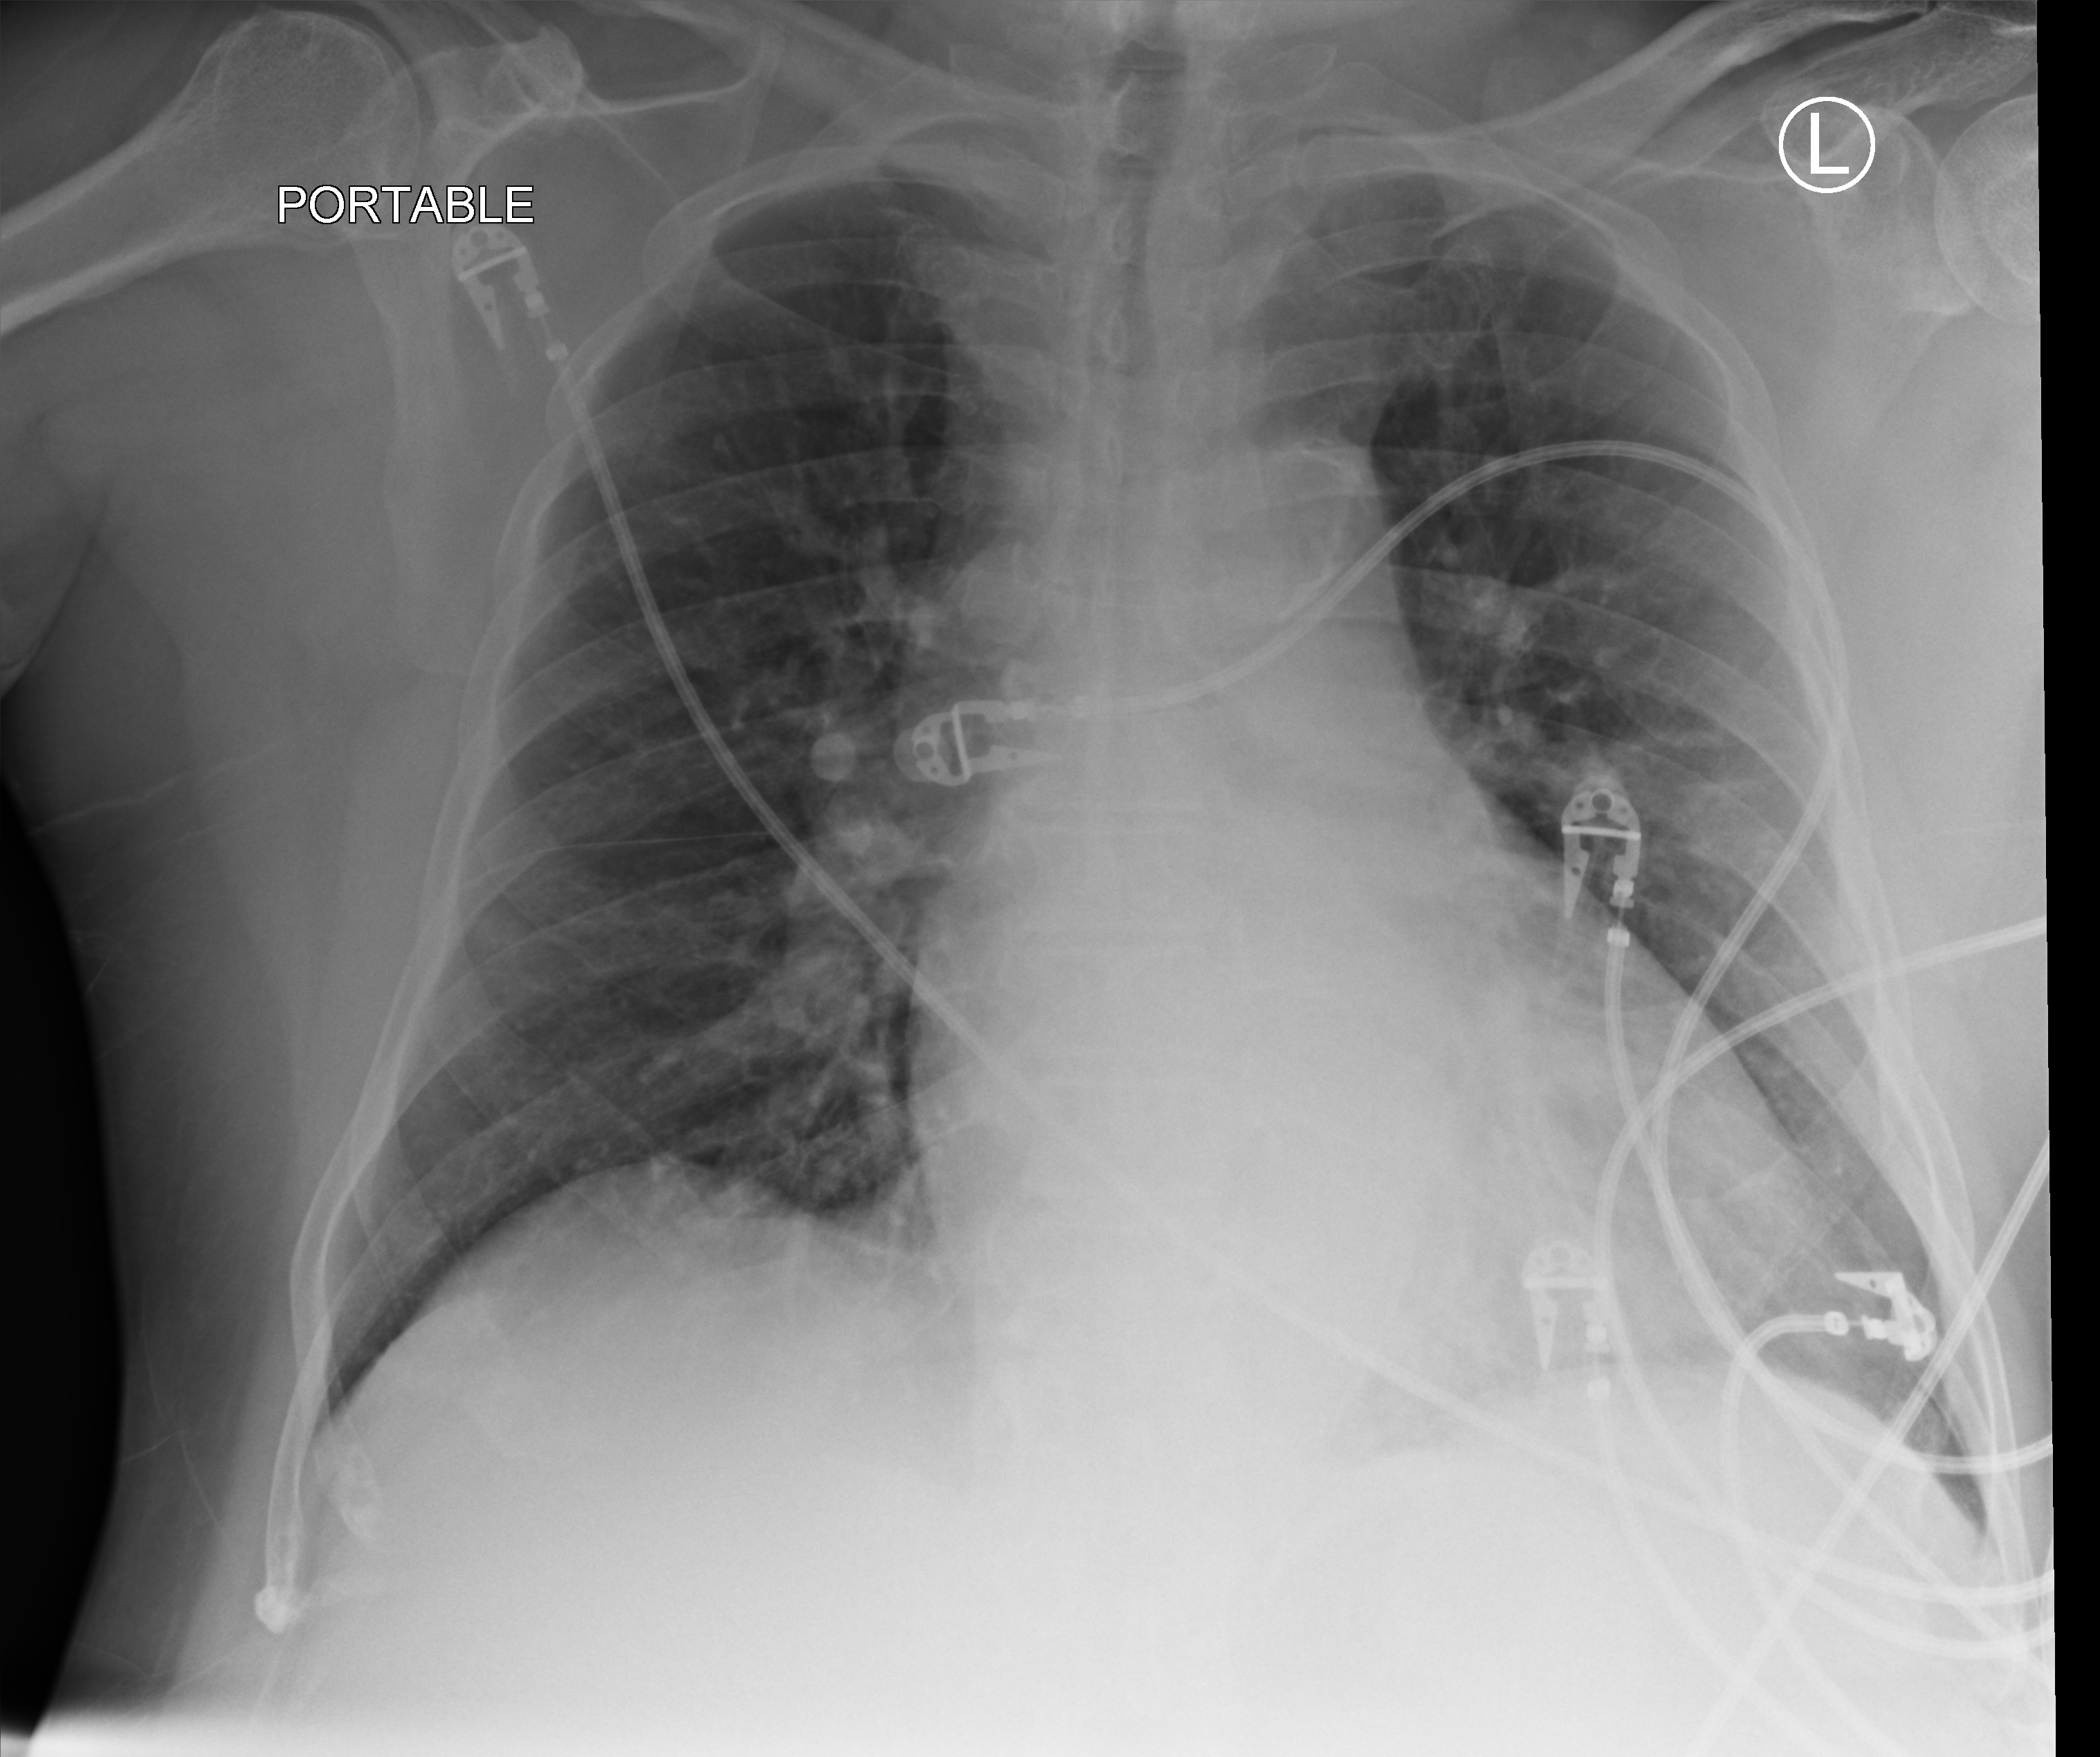
Portable chest radiograph; anteroposterior (AP) projection. Patient hospitalised with COVID-19; male, aged 60–74 years.
Admission-level facts for this patient (not findings on this image; timing relative to this image not recorded): mechanically ventilated during this hospital stay: no.